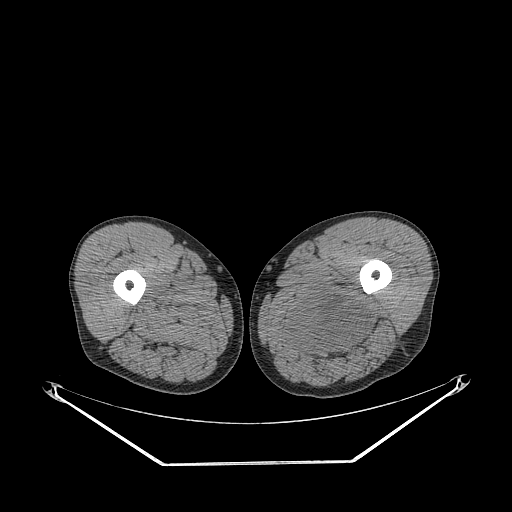
CT of an extremity soft-tissue mass (from a PET/CT study), one axial slice. Position 255 of 267 along the scan axis. Reconstruction kernel STANDARD. Soft-tissue window (W 400 / L 40 HU). 512 × 512 image matrix, field of view 500 × 500 mm. Male patient. From the clinical record (not read from this slice): histological type: undifferentiated pleomorphic liposarcoma; grade: high; site of the primary tumour: left thigh.
Annotated regions visible in this slice (expert contour drawn on MRI and transferred to this co-registered scan by the dataset authors):
- gross tumour volume including surrounding oedema: bounding box (x1, y1, x2, y2) in pixels: (281, 292, 369, 357)
- gross tumour volume (mass): (290, 295, 364, 352)